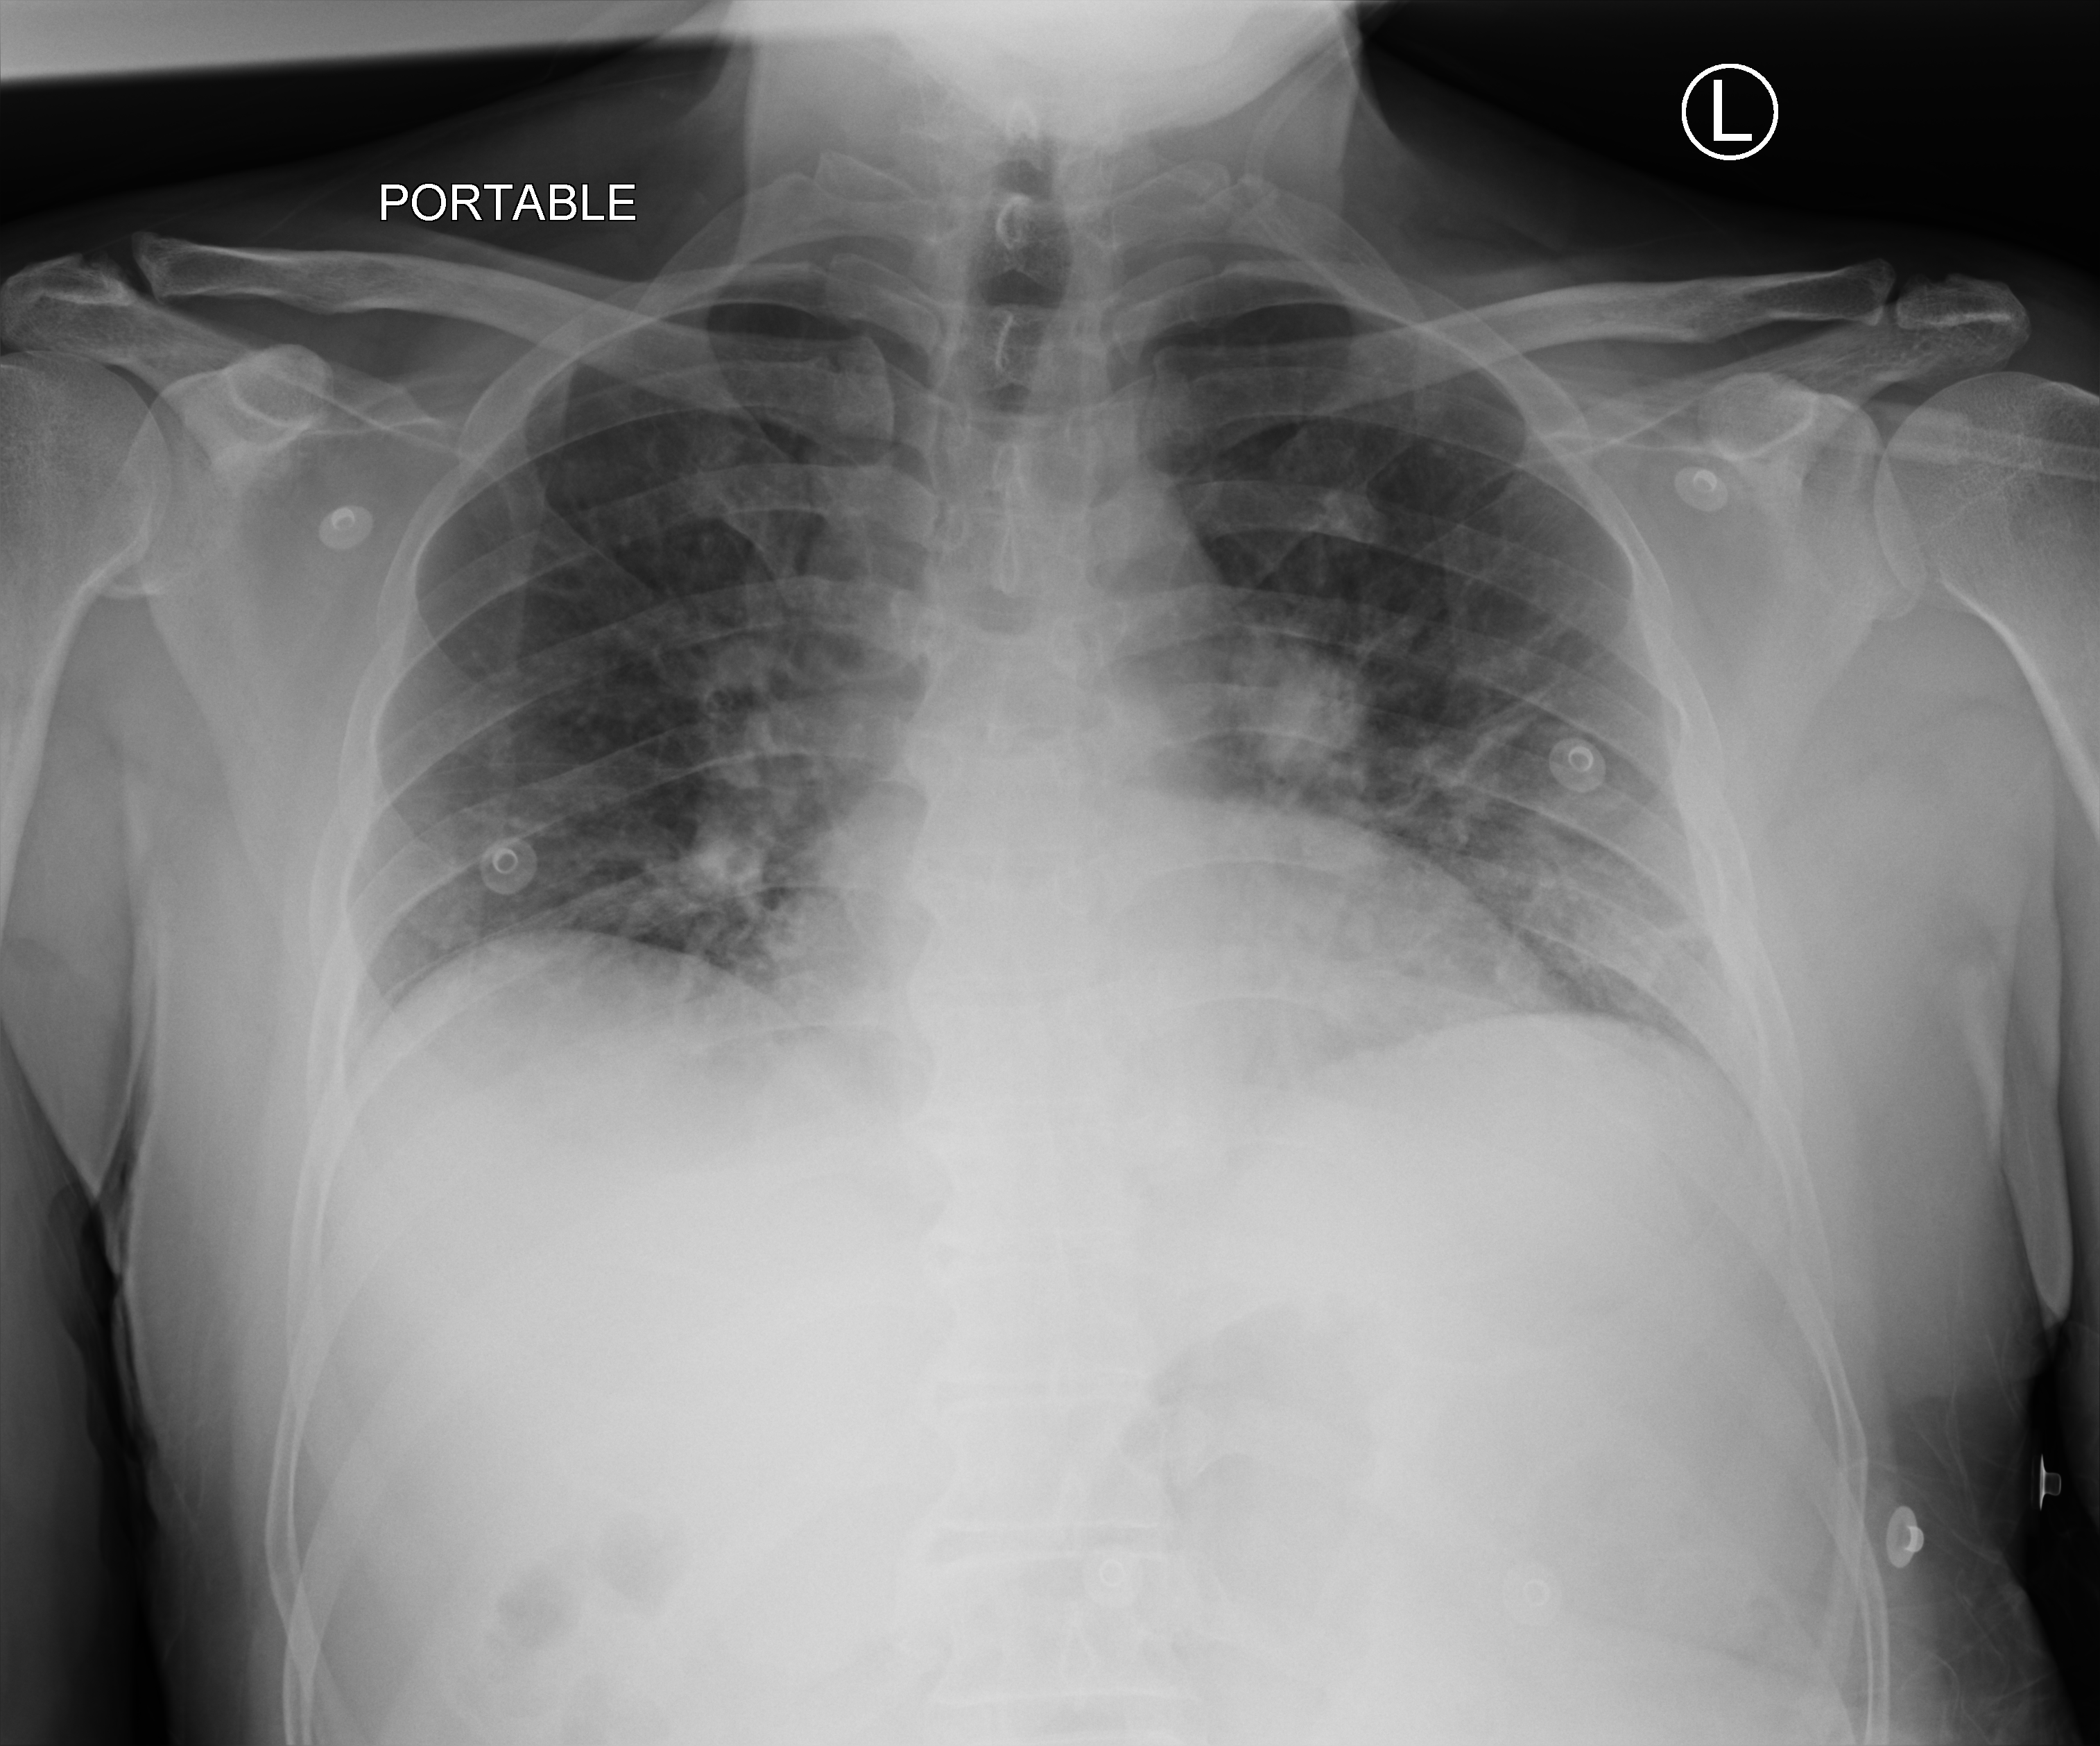
Chest X-ray (portable); anteroposterior (AP) projection. Male patient hospitalised with COVID-19, age 18–59 years.
Admission-level facts for this patient (not findings on this image; timing relative to this image not recorded):
- admitted to intensive care during this hospital stay: no
- mechanically ventilated during this hospital stay: no